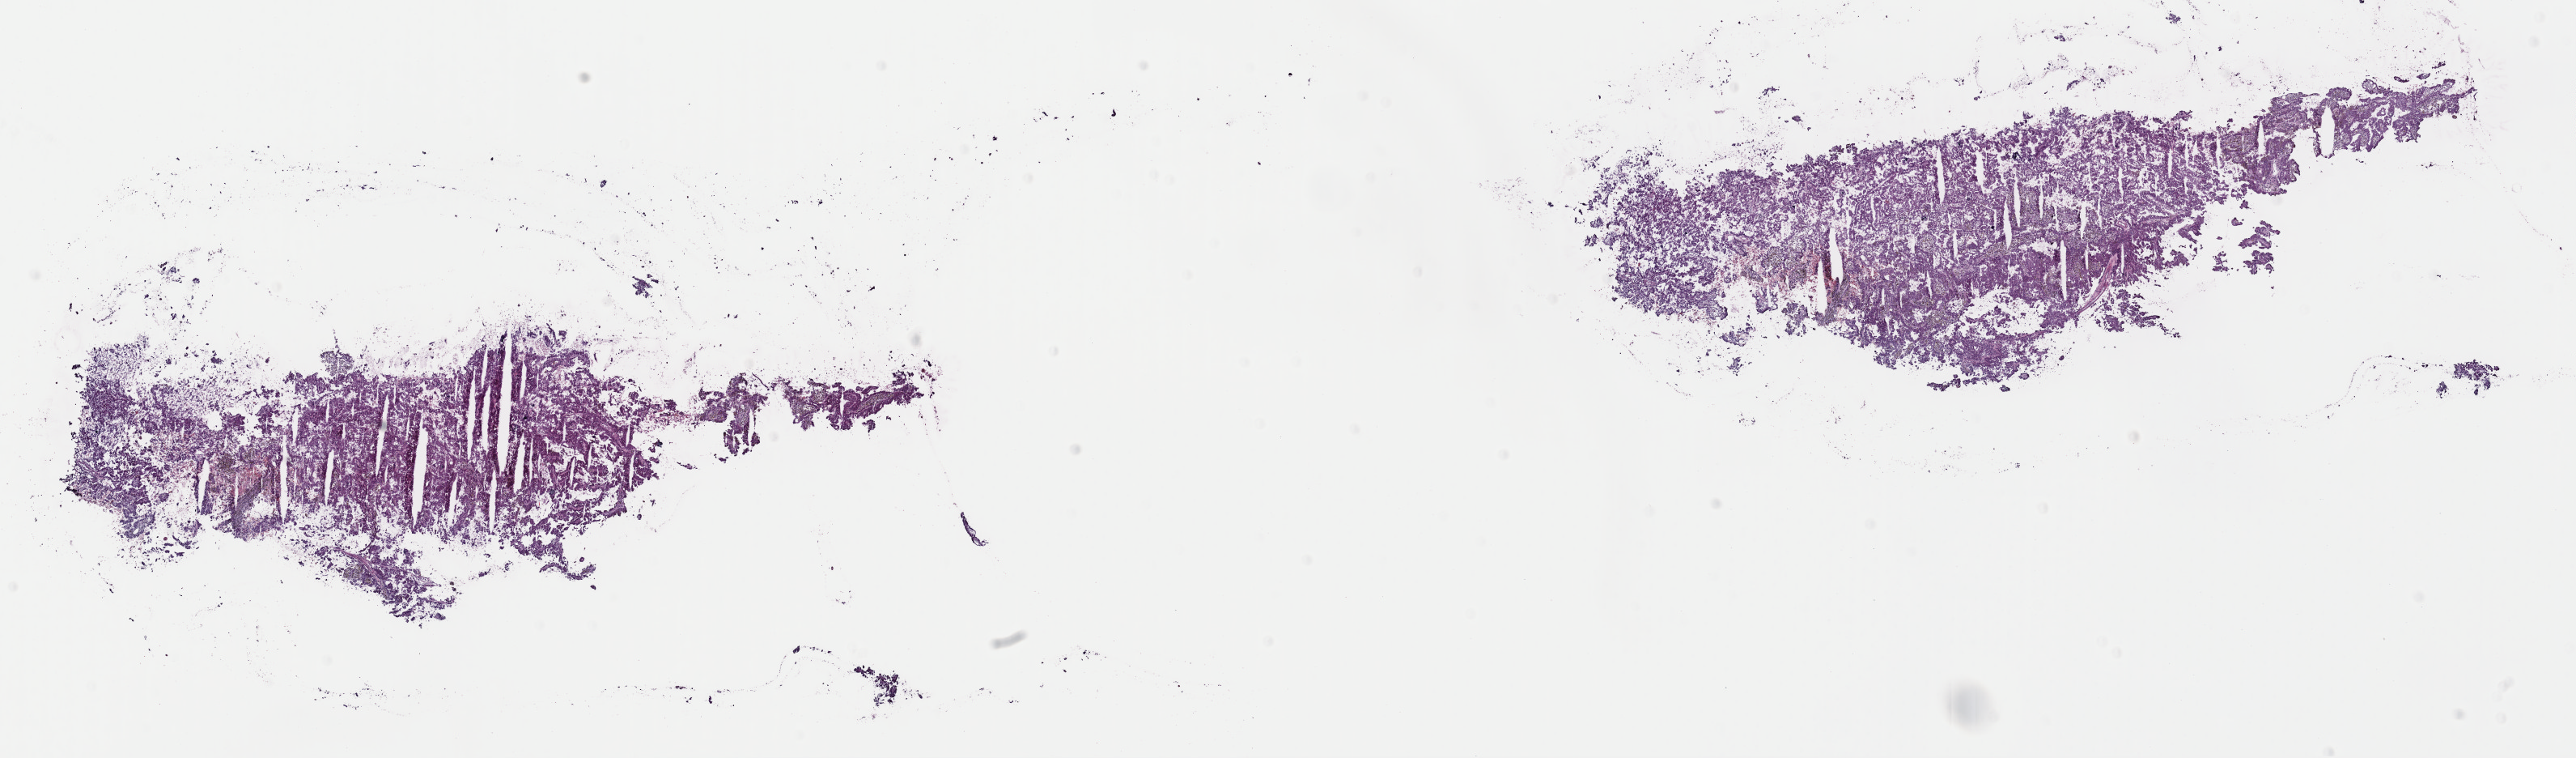
Digitized H&E-stained tissue section (whole slide) — whole scanned area (about 25.1 x 7.4 mm, slide scanned at 40x) shown as a low-resolution overview, frozen section from the top of the tissue portion, kidney, primary tumour sample. Male, age 84 years at initial diagnosis. Slide review estimates, as recorded: tumour cells 90%, tumour nuclei 100%, normal cells 0%, stromal cells 10%, necrosis 0%. Infiltration values recorded for this section: lymphocyte infiltration 0%, monocyte infiltration 10%, neutrophil infiltration 0%.
AJCC pathologic stage: I (7th edition). Pathologic diagnosis: Papillary adenocarcinoma, NOS.